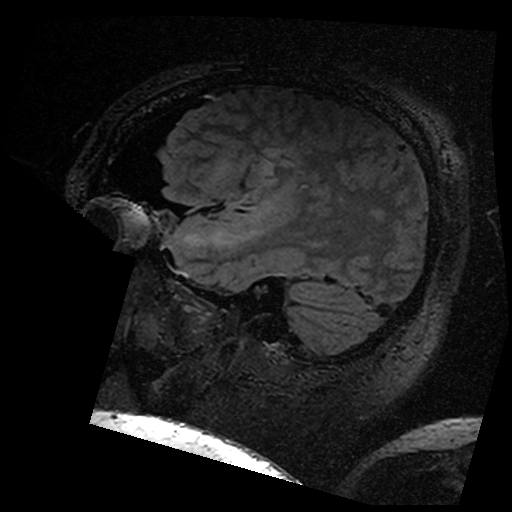
Brain MRI from a brain-tumour surgery series, one sagittal slice; position 129 of 176 along the scan axis; T2 FLAIR; 1 mm slice thickness; 512 × 512 image matrix, field of view 250 × 250 mm. Case-level facts recorded for this patient, not image findings: histopathology: Astrocytoma; WHO grade: 3; IDH mutation: yes; tumour location: Left Insular.
Annotated regions visible in this slice (outlined manually by an expert reader):
- residual tumour: box from (x=268, y=156) to (x=294, y=181) px